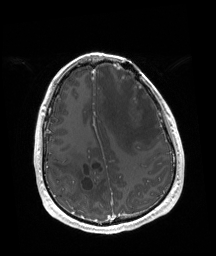
Brain MRI from a brain-tumour surgery series, one axial slice; position 54 of 192 along the scan axis; T1-weighted post-contrast; 1 mm slice thickness; 216 × 256 image matrix, field of view 219 × 260 mm. From the clinical record (not read from this slice): tumour location: Left Frontal.
Outlined on this slice (outlined manually by an expert reader):
- tumour: bounding box [x1, y1, x2, y2] px = [126, 70, 130, 74]